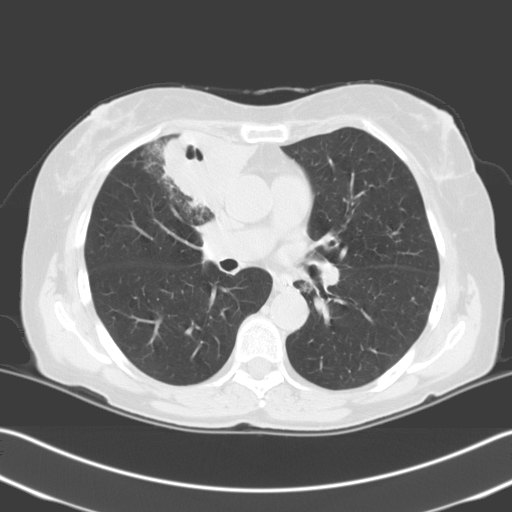
Low-dose screening chest CT, one axial slice; 140 kVp; lung window (W 1500 / L -600 HU); 3.2 mm slice thickness; 512 × 512 image matrix.
Annotated regions visible in this slice (expert manual segmentation):
- lesion 1 (tumor, upper lobe of right lung): bounding box <160,132,256,209> (left, top, right, bottom; pixels)